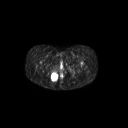
FDG PET of an extremity soft-tissue mass (from a PET/CT study), one axial slice. Slice 30 of 267 in the series (ordered by position). 3.27 mm slice thickness. 128 × 128 image matrix, field of view 700 × 700 mm. Female patient, age 17 years. From the clinical record (not read from this slice): histological type: epithelioid sarcoma; grade: intermediate; site of the primary tumour: right buttock.
Annotated regions visible in this slice (expert contour drawn on MRI and transferred to this co-registered scan by the dataset authors):
- gross tumour volume including surrounding oedema: bounding box <49,71,59,82> (left, top, right, bottom; pixels)
- gross tumour volume (mass): <50,73,58,81>